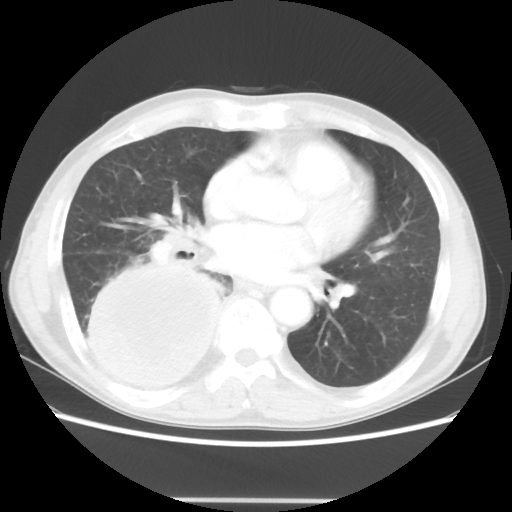
Chest CT, one axial slice; reconstruction kernel STANDARD; 100 kVp; lung window (W 1500 / L -600 HU); 5 mm slice thickness; 512 × 512 image matrix. Male patient, age 66 years. From the clinical record (not read from this slice): clinical TNM (as recorded): T4 N1 M1; histopathological grade: G3.
Structures marked on this image (bounding box drawn by a radiologist):
- lung tumour (recorded histology: small cell carcinoma): bounding box <85,254,231,406> (left, top, right, bottom; pixels)